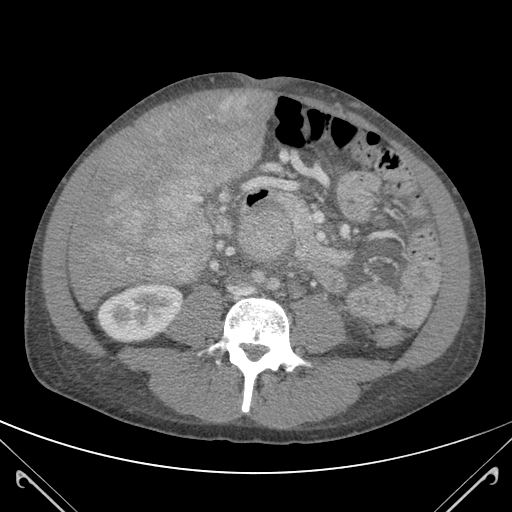
Contrast-enhanced abdominal CT (liver protocol), one axial slice; position 37 of 118 along the scan axis; 120 kVp; soft-tissue window (W 400 / L 40 HU); 512 × 512 image matrix. From the clinical record (not read from this slice): diagnosis: hepatocellular carcinoma (patient treated with transarterial chemoembolisation; whether this scan precedes or follows treatment is not stated here); TNM stage (as recorded): Stage-IIIB; Child-Pugh class: A; tumour nodularity: uninodular.
Structures marked on this image (semi-automatic segmentation, software-assisted and operator-edited):
- mass: bounding box [x1, y1, x2, y2] px = [89, 91, 263, 286]